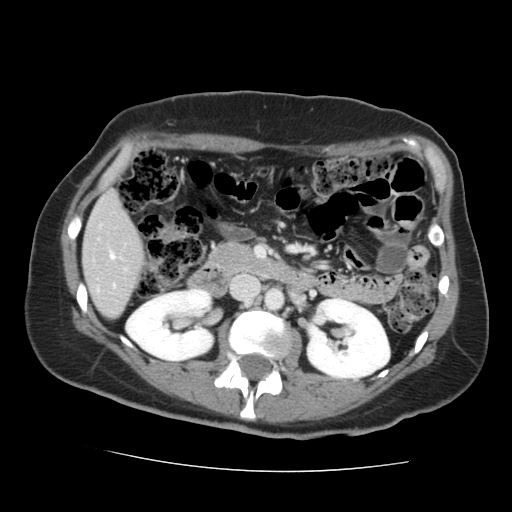
Contrast-enhanced abdominal CT, one axial slice. Position 61 of 144 along the scan axis. 120 kVp. Intravenous contrast given. Soft-tissue window (W 400 / L 40 HU). 2.5 mm slice thickness. 512 × 512 image matrix, field of view 333 × 333 mm. Female patient, age 46 years. Case-level facts recorded for this patient, not image findings: diagnosis: colorectal cancer liver metastases, imaged before liver resection; multiple liver metastases: no; largest metastasis: 2.8 cm; disease in both lobes: no.
Annotated regions visible in this slice (outlined manually by an expert reader):
- liver: bounding box <84,194,142,317> (left, top, right, bottom; pixels)
- planned liver remnant (the part of the liver to remain after resection): <84,194,142,259>
- portal vein (with intrahepatic branches): <110,254,114,286>